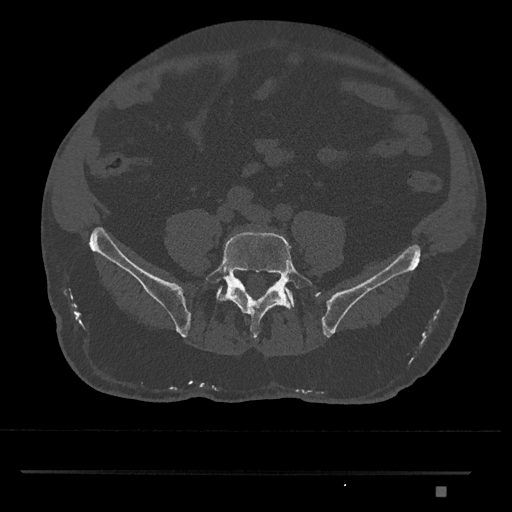
CT including the spine, one axial slice. Position 555 of 1134 along the scan axis. Reconstruction kernel Br40s/3. Bone window (W 1800 / L 400 HU). 0.5 mm slice thickness. 512 × 512 image matrix, field of view 429 × 429 mm. Male patient, age 65 years. From the clinical record (not read from this slice): primary cancer: prostate.
Structures marked on this image (semi-automatically segmented with operator editing):
- L5 vertebra: bounding box [x1, y1, x2, y2] px = [205, 231, 314, 340]